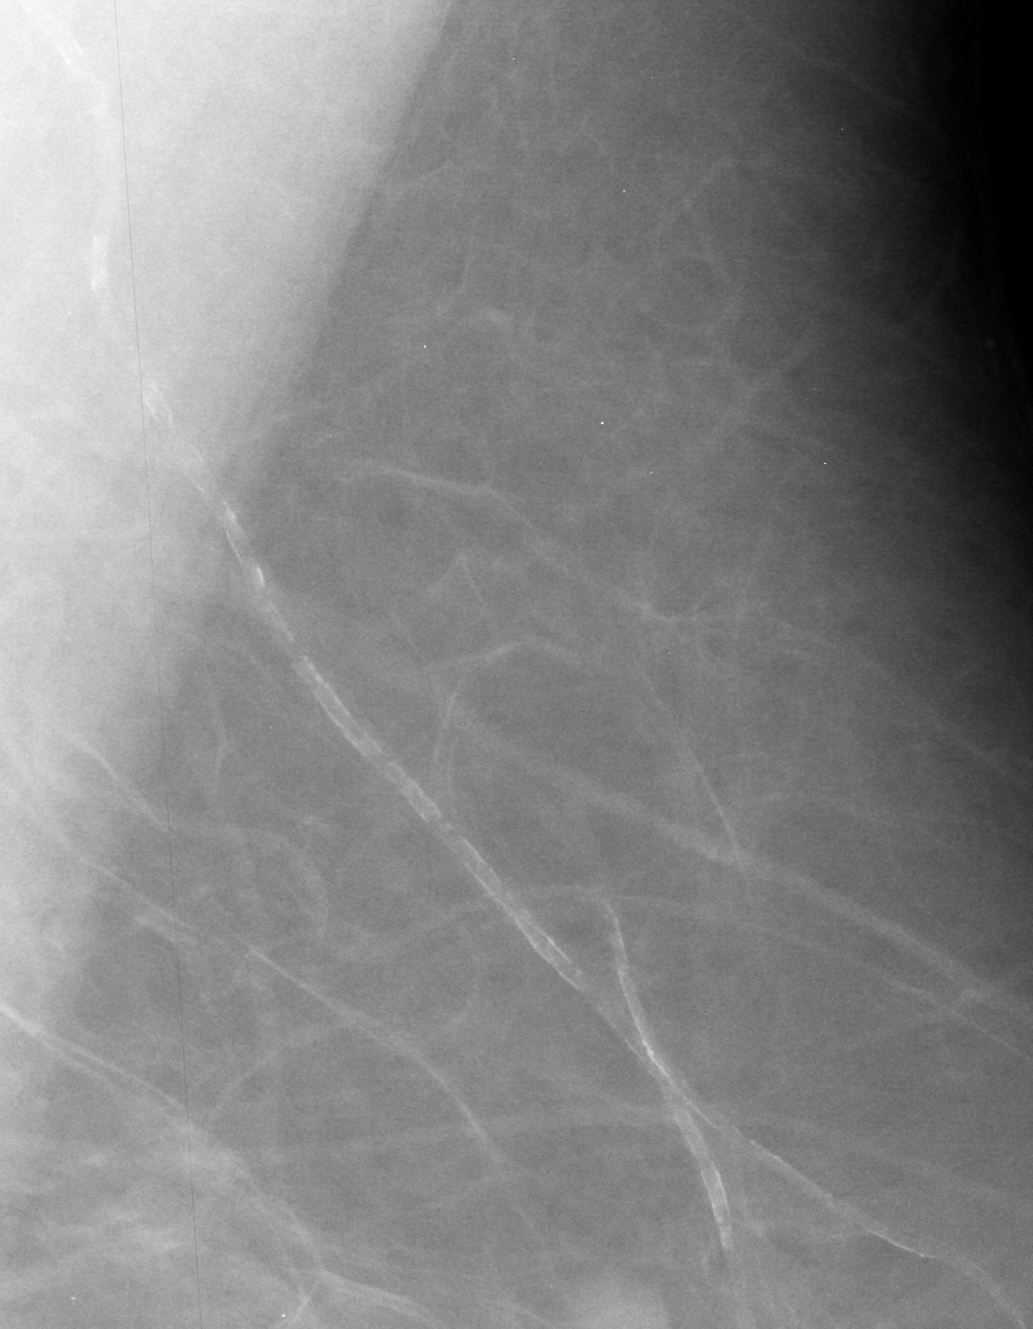
Region of interest cut from a scanned film mammogram (one marked finding); left breast; MLO view; BI-RADS breast density category 1 (scale 1–4).
- Marked abnormality: calcifications, morphology vascular; BI-RADS assessment category 2; benign without callback (not worked up further).